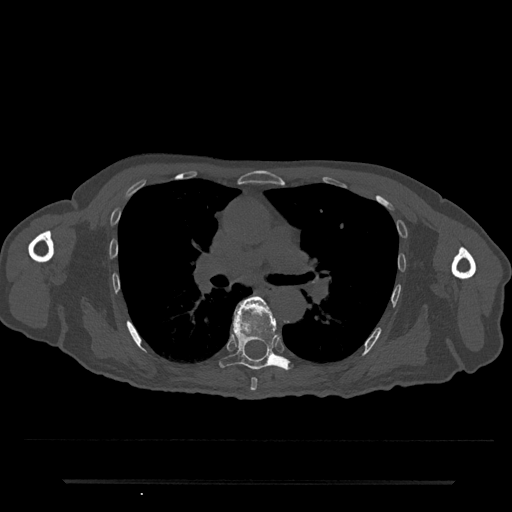
CT including the spine, one axial slice. Position 491 of 797 along the scan axis. 120 kVp. Bone window (W 1800 / L 400 HU). 0.5 mm slice thickness. 512 × 512 image matrix. Patient: male, 74 years. From the clinical record (not read from this slice): primary cancer: prostate.
Annotated regions visible in this slice (semi-automatic segmentation, software-assisted and operator-edited):
- T6 vertebra: box from (x=244, y=297) to (x=265, y=391) px
- T7 vertebra: (x=219, y=300)–(x=293, y=370)